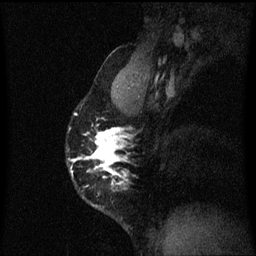
Breast MRI (dynamic contrast-enhanced), one sagittal slice. Slice 42 of 60 in the series (ordered by position). Dynamic contrast-enhanced series, image 2 of 3 at this slice position (ordered by acquisition). 1.5 T. TE 4.2 ms, TR 8.4 ms. 2 mm slice thickness. 256 × 256 image matrix, field of view 200 × 200 mm. Female patient, age 40 years.
Annotated regions visible in this slice (semi-automatic segmentation, software-assisted and operator-edited):
- analysis volume of interest (the breast-tissue region the enhancement analysis was run in; not a lesion): bounding box (x1, y1, x2, y2) in pixels: (68, 114, 126, 211)
- tumour enhancement mask (voxels above the 70 % enhancement threshold inside the analysis volume of interest): (71, 114, 124, 185)